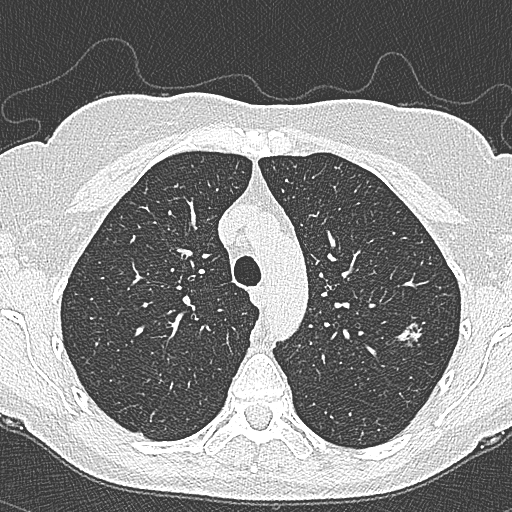
Low-dose screening chest CT, axial slice, second annual screen, lung window (W 1500 / L -600 HU), 1 mm slice thickness, slice 86 of 350 in the series. Female participant, aged 65 years at enrolment. Current smoker at enrolment.
Expert-annotated lung lesion, bounding box <394,310,441,358> (left, top, right, bottom; pixels). The screening reader recorded 4 non-calcified nodules or masses ≥4 mm on this exam (left upper lobe, left upper lobe, left upper lobe, right lower lobe); which of them this box marks is not recorded.